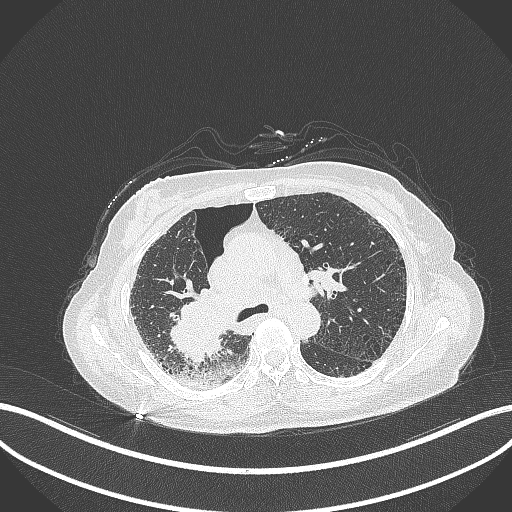
Chest CT, one axial slice; position 224 of 408 along the scan axis; lung window (W 1500 / L -600 HU); 1 mm slice thickness; 512 × 512 image matrix, field of view 400 × 400 mm. Patient: female, 64 years. From the clinical record (not read from this slice): clinical TNM (as recorded): T3 N3 M0.
Outlined on this slice (rectangle marked by the reading radiologist):
- lung tumour (recorded histology: squamous cell carcinoma): bounding box (x1, y1, x2, y2) in pixels: (161, 288, 234, 369)